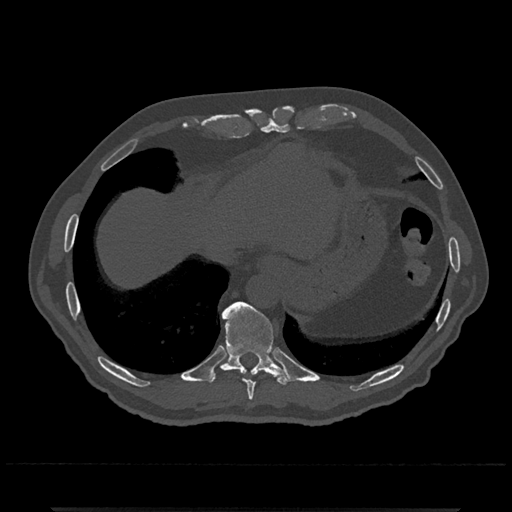
CT including the spine, one axial slice. Slice 575 of 797 in the series (ordered by position). Reconstruction kernel Br40s/3. 120 kVp. Bone window (W 1800 / L 400 HU). 0.5 mm slice thickness. 512 × 512 image matrix, field of view 393 × 393 mm. Male patient, age 67 years. Case-level facts recorded for this patient, not image findings: primary cancer: prostate.
Outlined on this slice (semi-automatically segmented with operator editing):
- T10 vertebra: bounding box (x1, y1, x2, y2) in pixels: (209, 301, 290, 386)
- T9 vertebra: (243, 379, 255, 401)